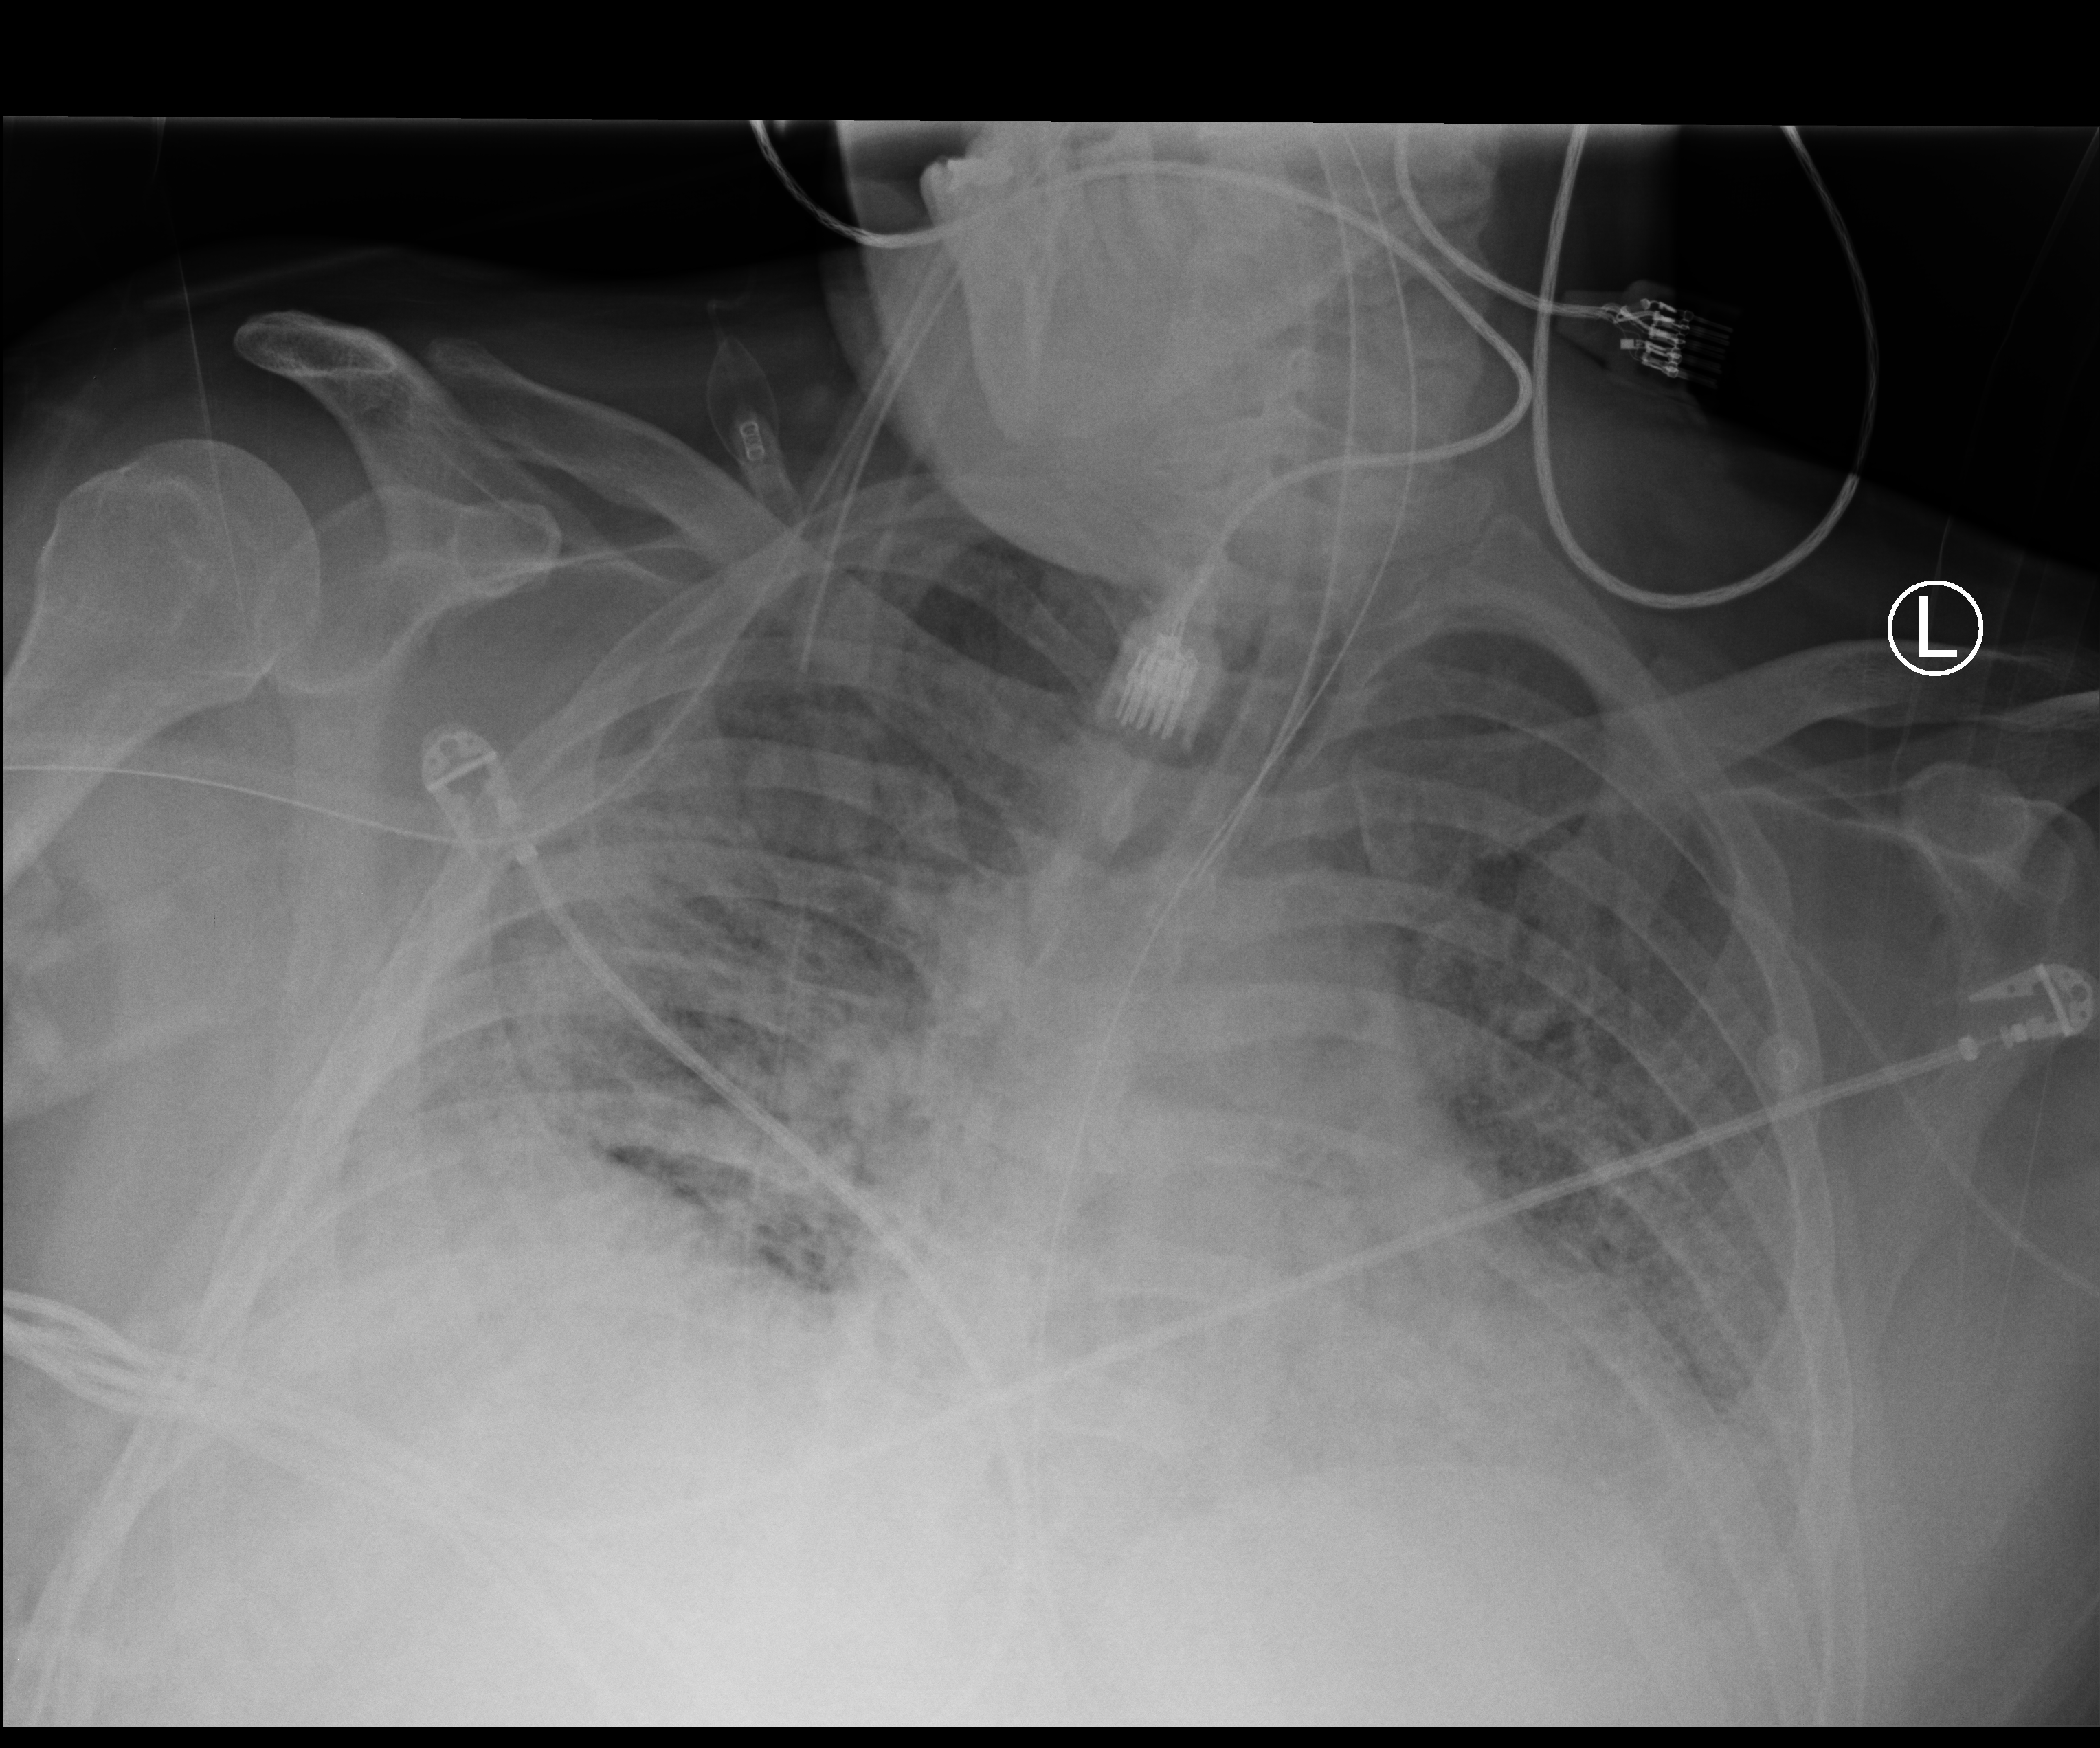
Bedside chest radiograph (computed radiography), anteroposterior (AP) projection. Male patient hospitalised with COVID-19, age 18–59 years.
Hospital-stay facts (about this admission, not read from this image; timing relative to this image not recorded):
- mechanically ventilated during this hospital stay: yes